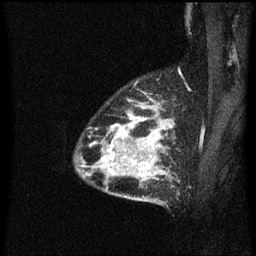
Breast MRI (dynamic contrast-enhanced), one sagittal slice. Position 48 of 60 along the scan axis. Dynamic contrast-enhanced series, image 2 of 3 at this slice position (ordered by acquisition). 1.5 T. TE 4.2 ms, TR 8.4 ms. 2 mm slice thickness. 256 × 256 image matrix, field of view 200 × 200 mm. Female patient, age 34 years. From the clinical record (not read from this slice): setting: breast cancer imaged before/during neoadjuvant chemotherapy; receptor status: HR-positive, HER2-negative.
Structures marked on this image (semi-automatically segmented with operator editing):
- analysis volume of interest (the breast-tissue region the enhancement analysis was run in; not a lesion): bounding box [x1, y1, x2, y2] px = [77, 100, 174, 205]
- tumour enhancement mask (voxels above the 70 % enhancement threshold inside the analysis volume of interest): [107, 114, 171, 175]